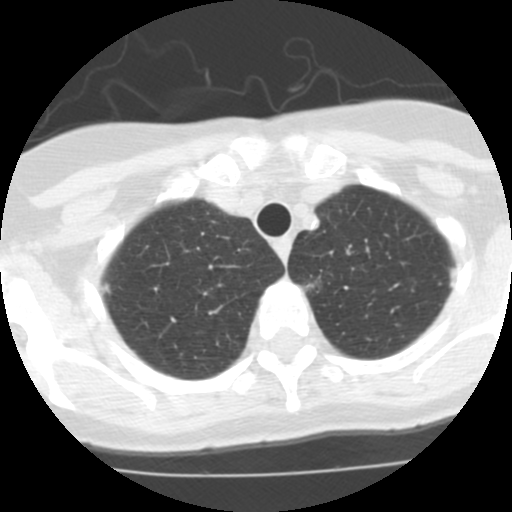
Low-dose screening chest CT, one axial slice. 120 kVp. Lung window (W 1500 / L -600 HU). 2.5 mm slice thickness. 512 × 512 image matrix.
Structures marked on this image (manually delineated by an expert):
- lesion 1 (tumor, upper lobe of left lung): bounding box (x1, y1, x2, y2) in pixels: (448, 269, 457, 288)